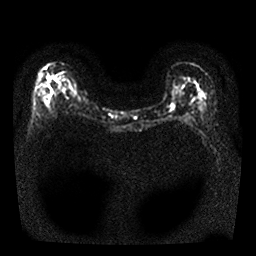
Breast MRI, one axial slice; position 14 of 25 along the scan axis; diffusion-weighted series; image 2 of 4 stored at this slice position (different b-values; order by instance number); 1.5 T; 4 mm slice thickness; 256 × 256 image matrix, field of view 300 × 300 mm. Female patient.
Outlined on this slice (outlined manually by an expert reader):
- tumour on diffusion-weighted imaging: box from (x=47, y=76) to (x=51, y=82) px